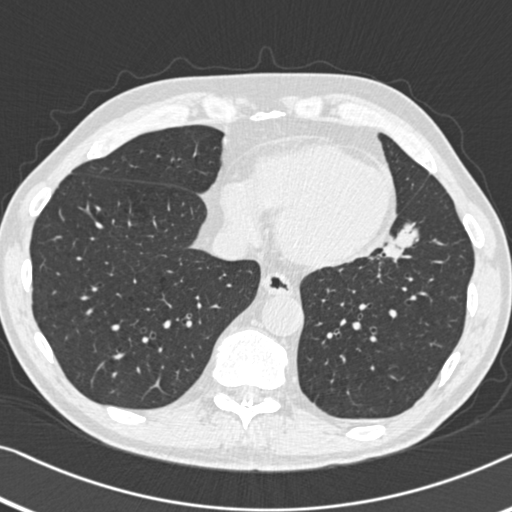
Low-dose screening chest CT, one axial slice; position 139 of 383 along the scan axis; reconstruction kernel B30f; 120 kVp; lung window (W 1500 / L -600 HU); 512 × 512 image matrix.
Outlined on this slice (expert manual segmentation):
- lesion 1 (tumor, upper lobe of left lung): bounding box (x1, y1, x2, y2) in pixels: (383, 223, 418, 261)